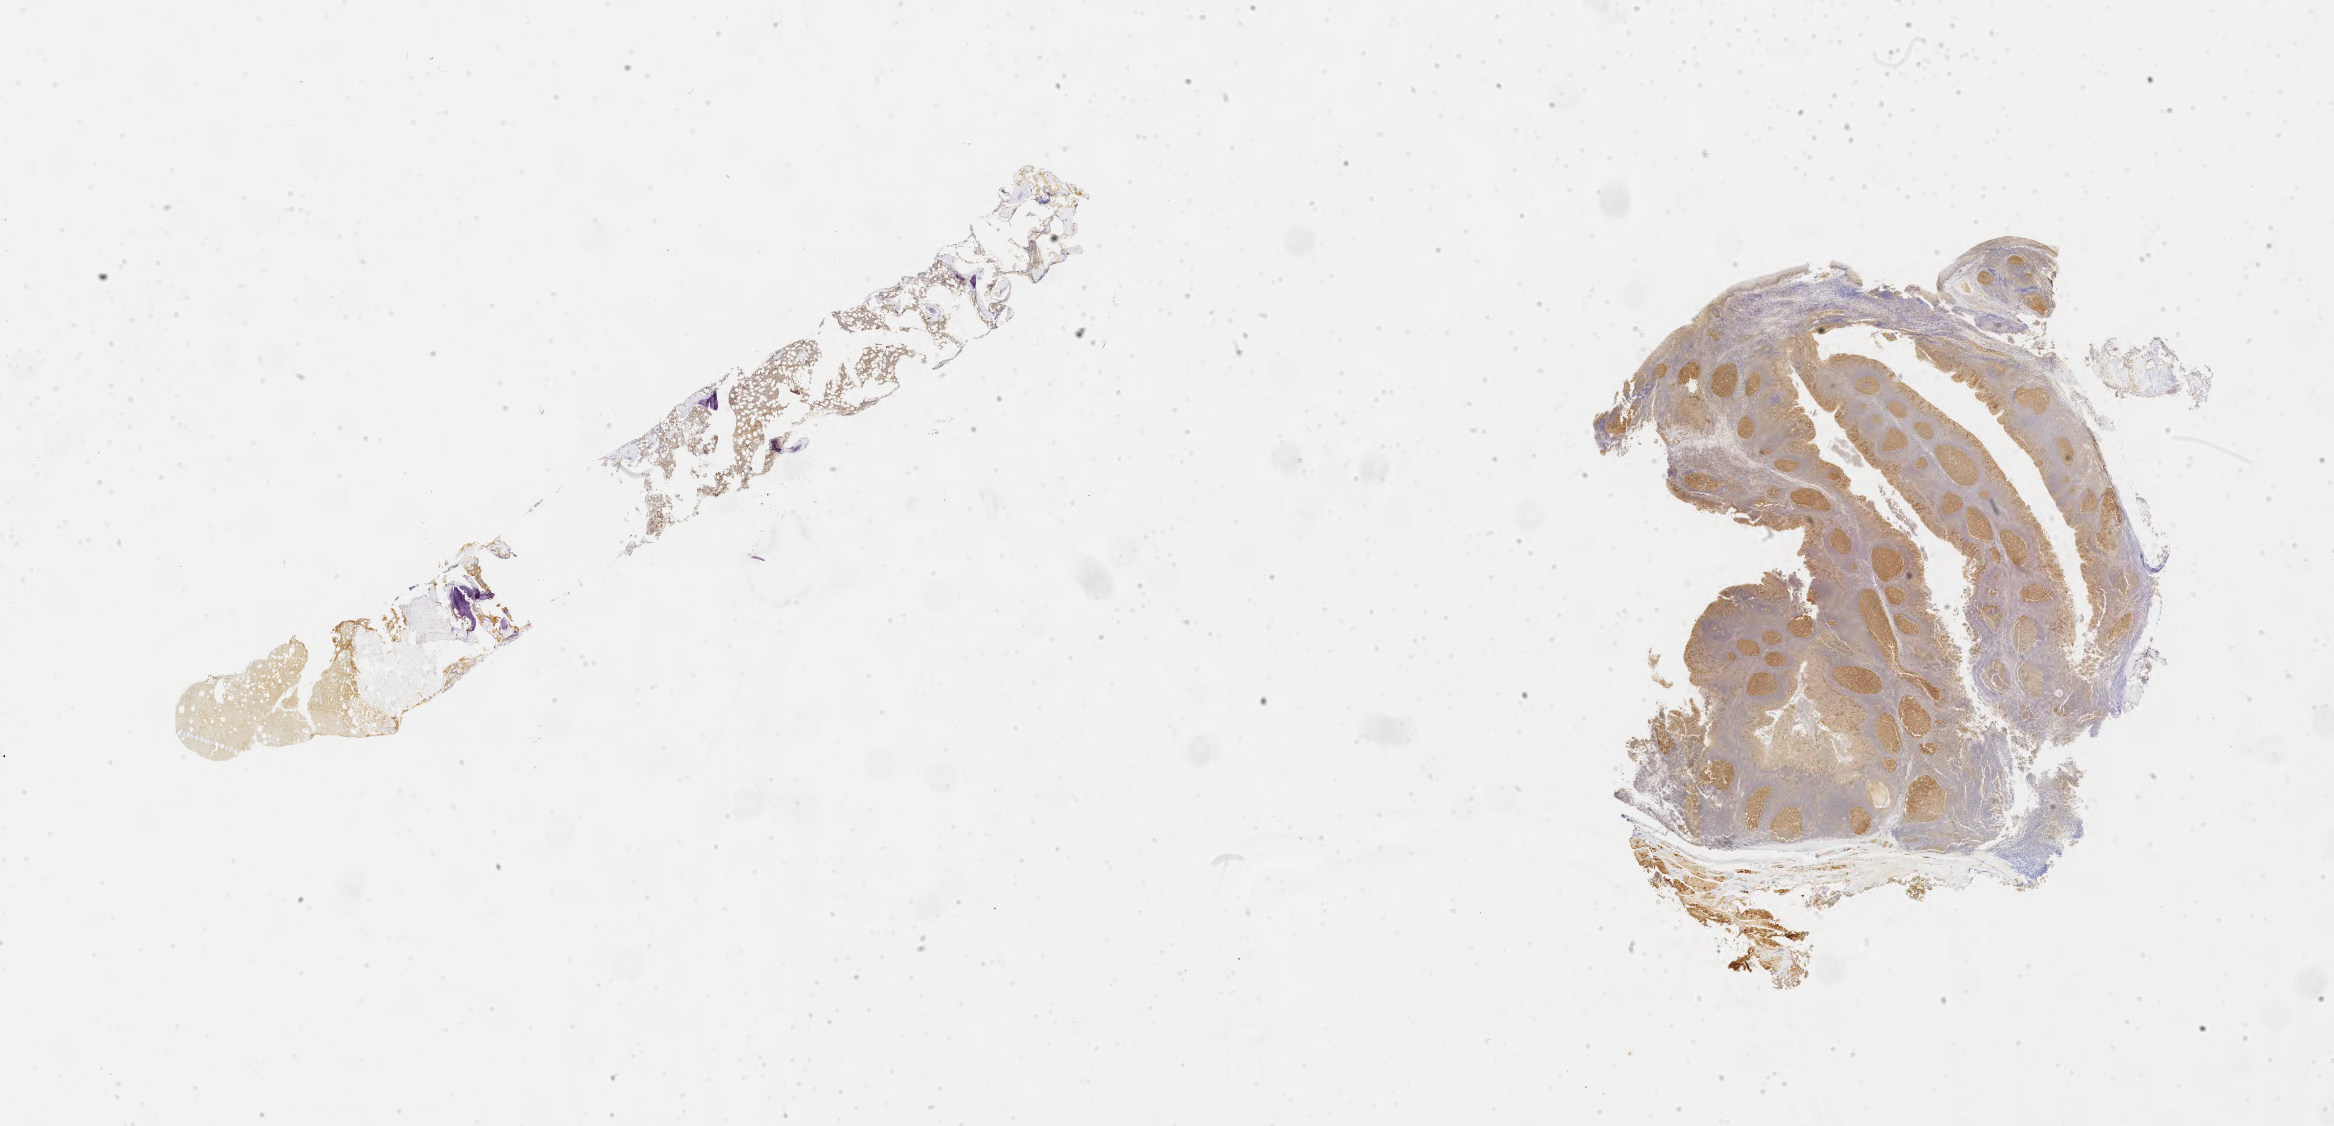
IHC for BCL6, whole-slide image — whole scanned area (about 37.7 x 18.2 mm) shown as a low-resolution overview. Specimen: tumor tissue. Site: bone marrow. Patient: male, aged 15.
* diagnosis: Burkitt lymphoma, NOS